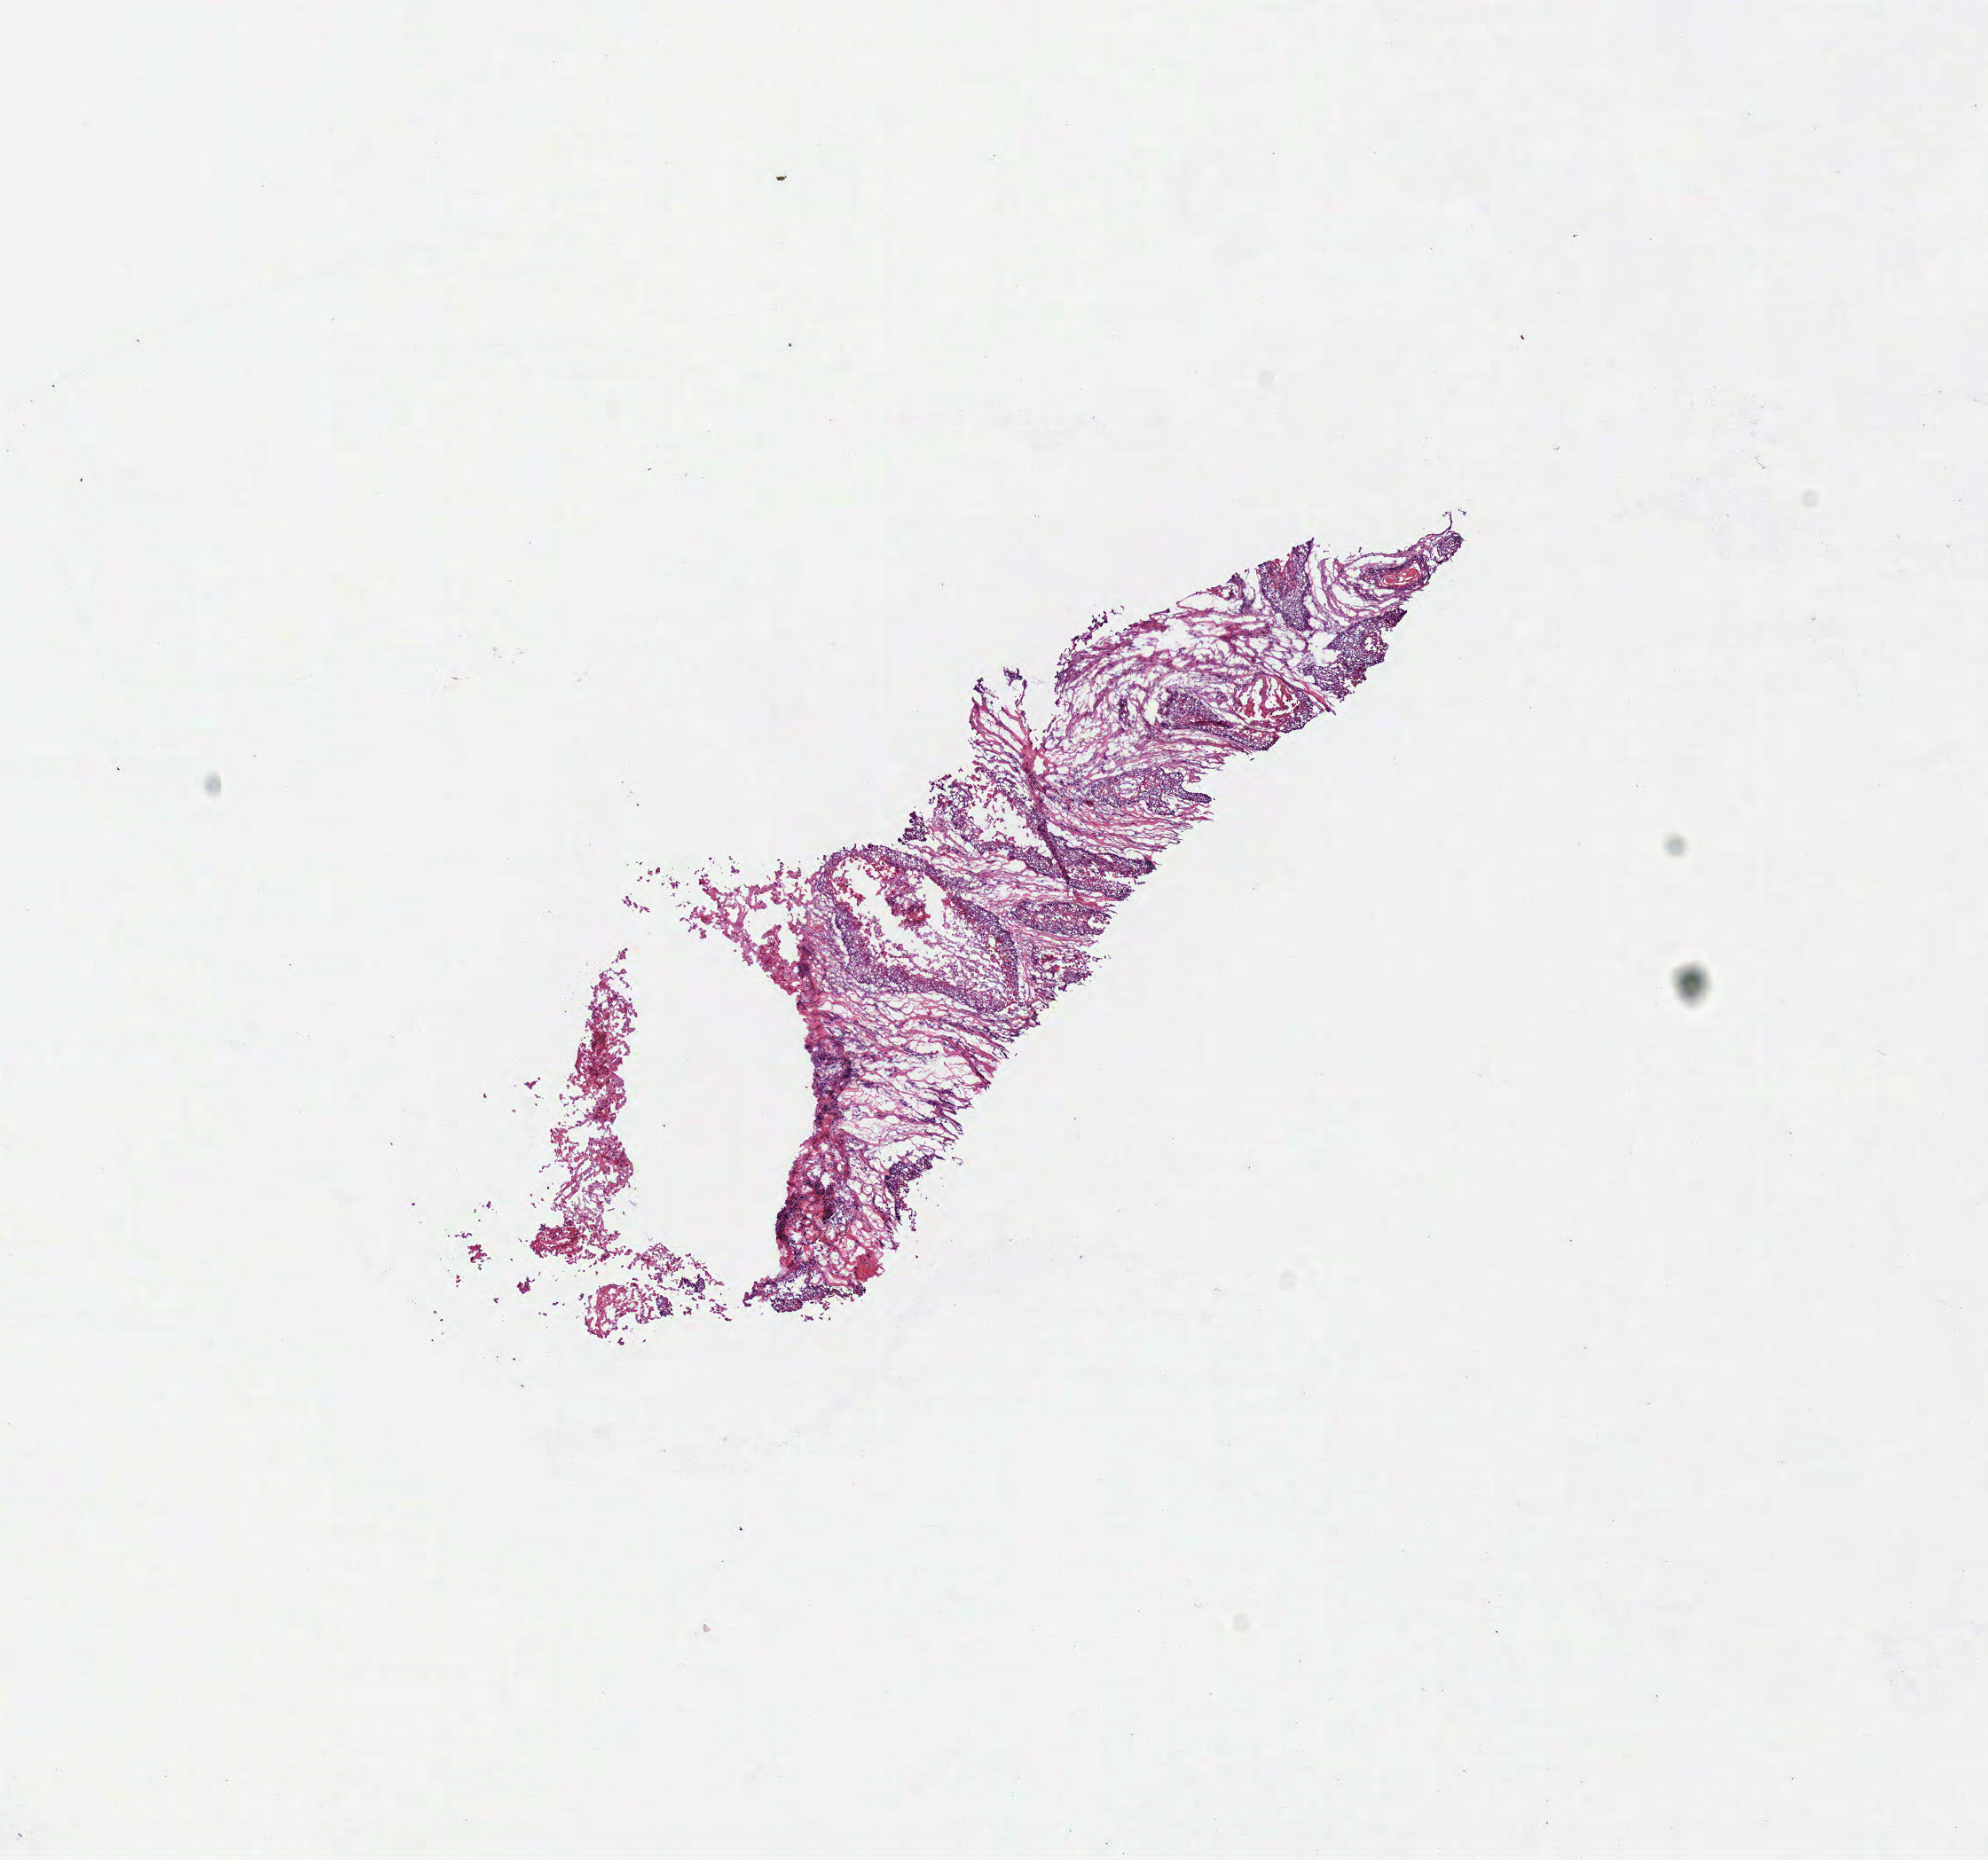
Whole-slide histology image, H&E — shown as a low-resolution overview of the whole scanned area (about 8.8 x 8.2 mm), frozen section from the top of the tissue portion, sample: primary tumour, head and neck. Male patient; age at initial diagnosis 80 years. Histologic grade: G2 (moderately differentiated). Pathologist review of this section (percent, as recorded): tumour cells 40%, tumour nuclei 70%, normal cells 0%, stromal cells 50%, necrosis 10%.
• AJCC pathologic stage: II (7th edition)
• diagnosis: Squamous cell carcinoma, NOS (larynx, NOS)